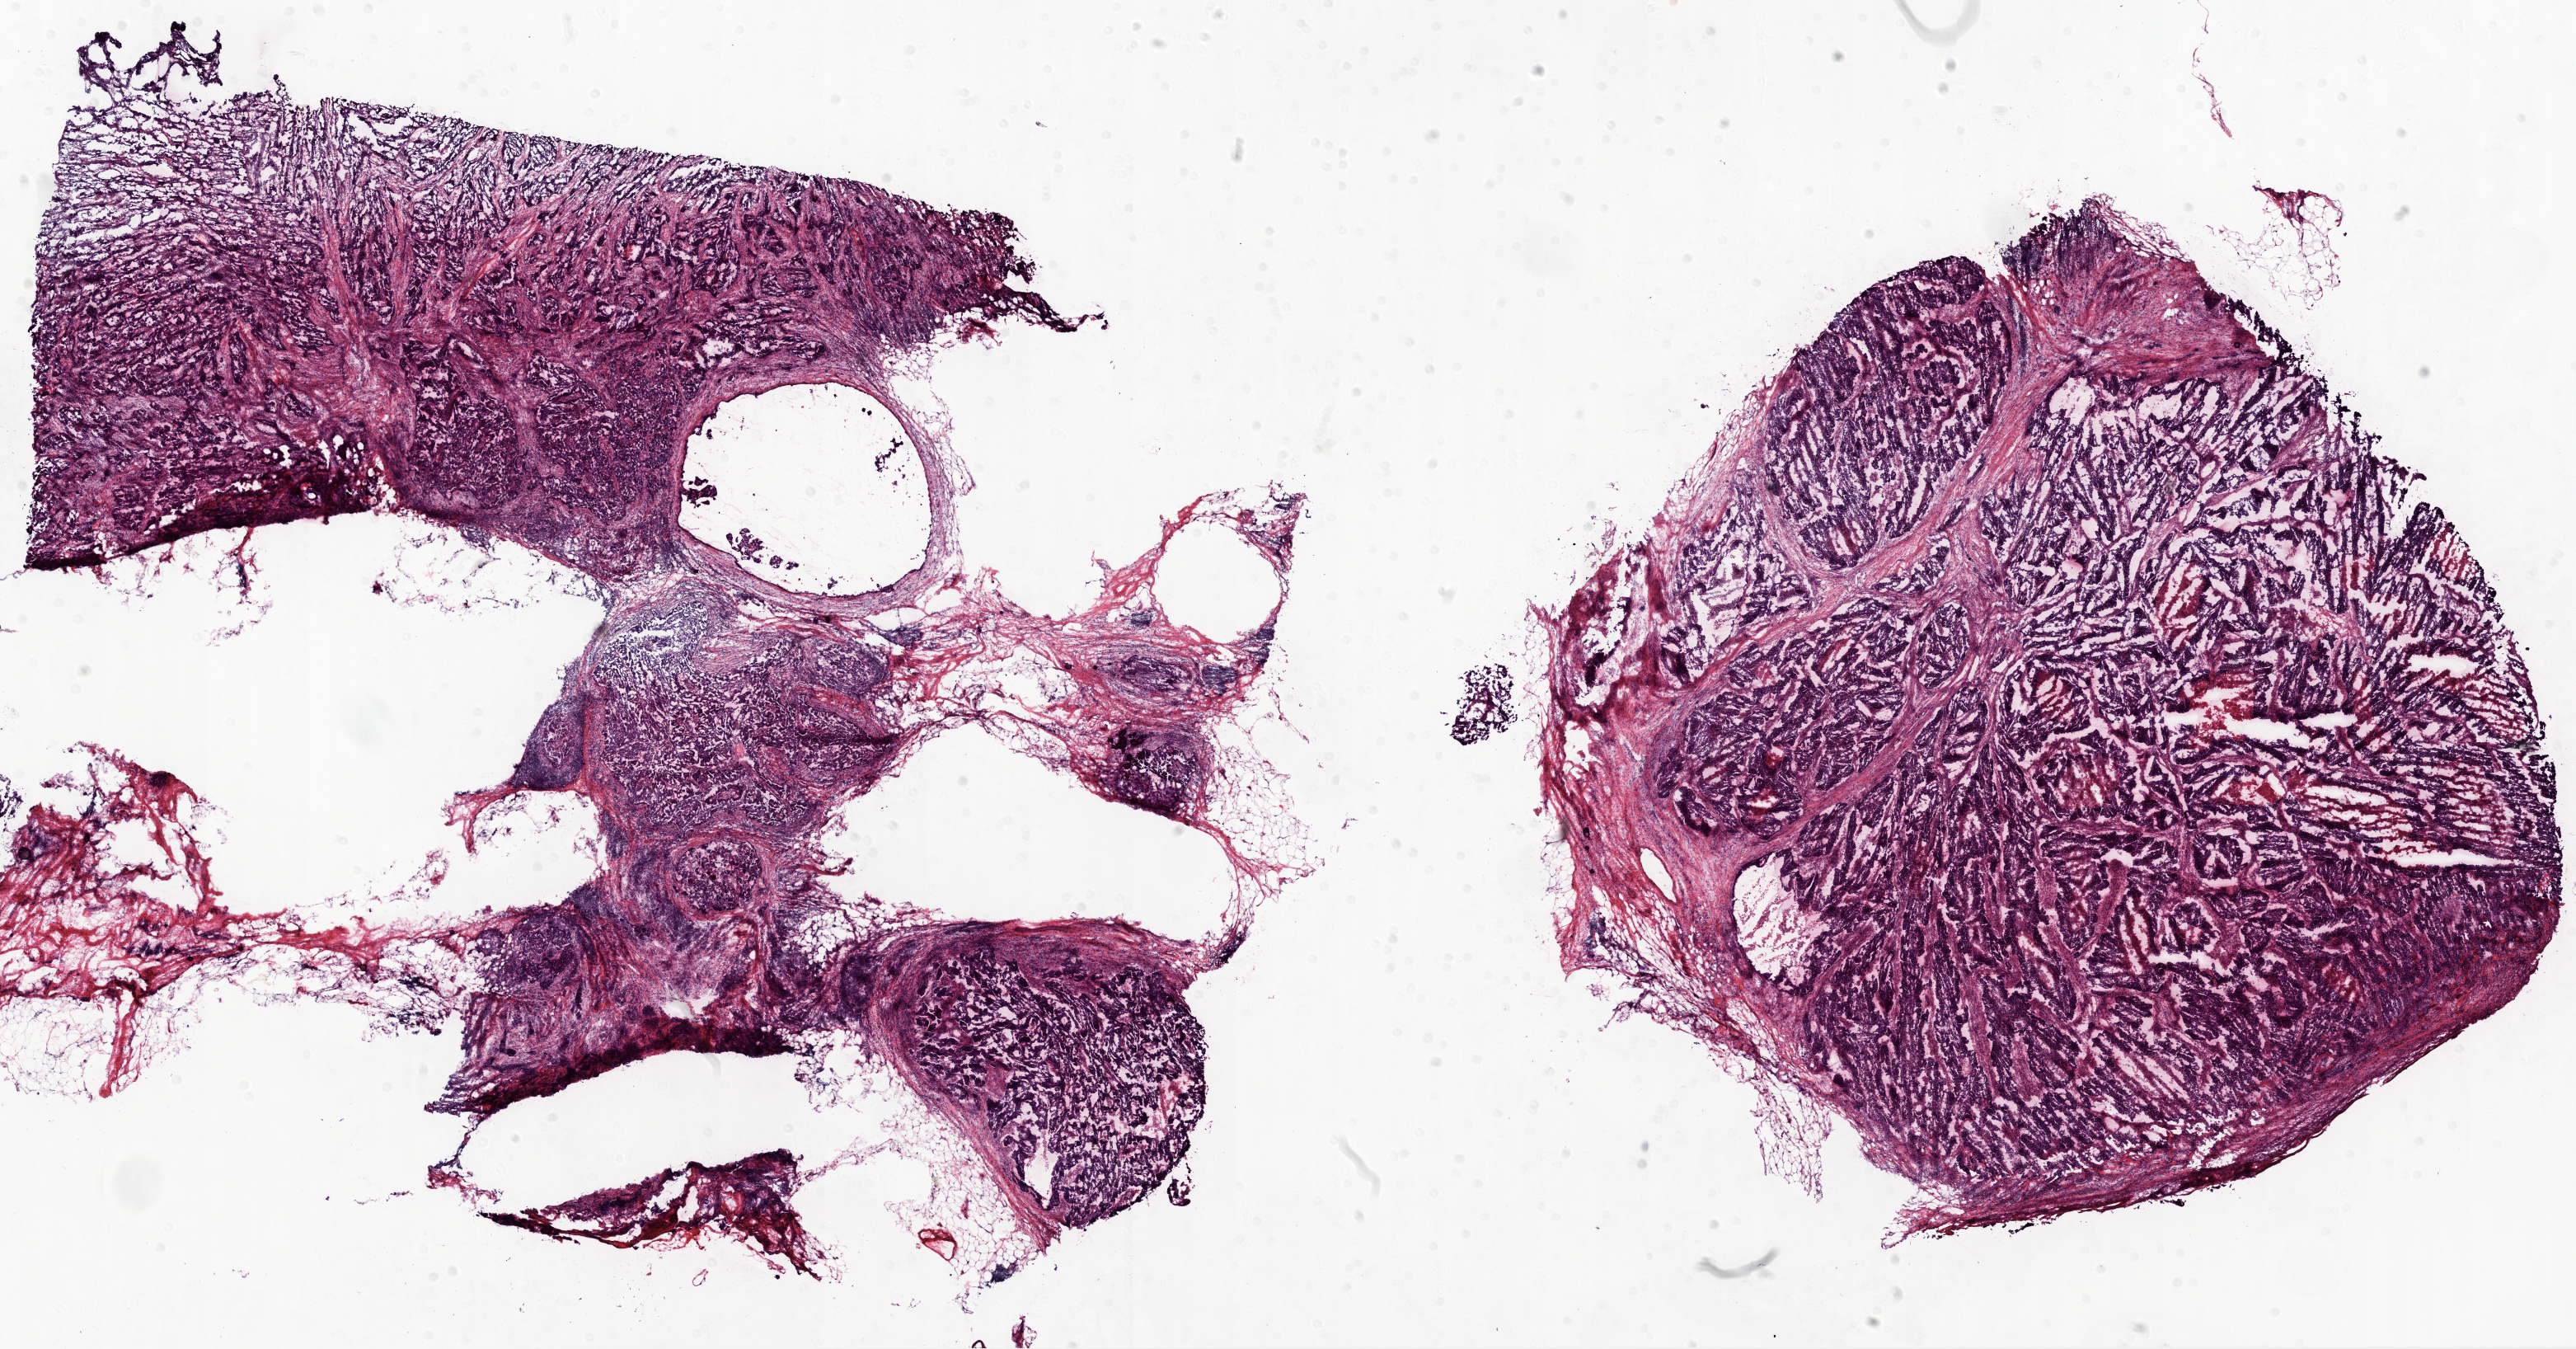
H&E whole-slide image, shown as a low-resolution overview of the whole scanned area (about 25.1 x 13.1 mm, slide scanned at 20x). Frozen section from the top of the tissue portion. Ovary, primary tumour sample. Female, age 59 years at initial diagnosis. Histologic grade: G3 (poorly differentiated). Pathologist review of this section (percent, as recorded): tumour cells 80%, tumour nuclei 95%, normal cells 0%, stromal cells 15%, necrosis 5%. Infiltration values recorded for this section: lymphocyte infiltration 95%, neutrophil infiltration 5%.
- FIGO stage: IV
- laterality: bilateral
- diagnosis: Serous cystadenocarcinoma, NOS